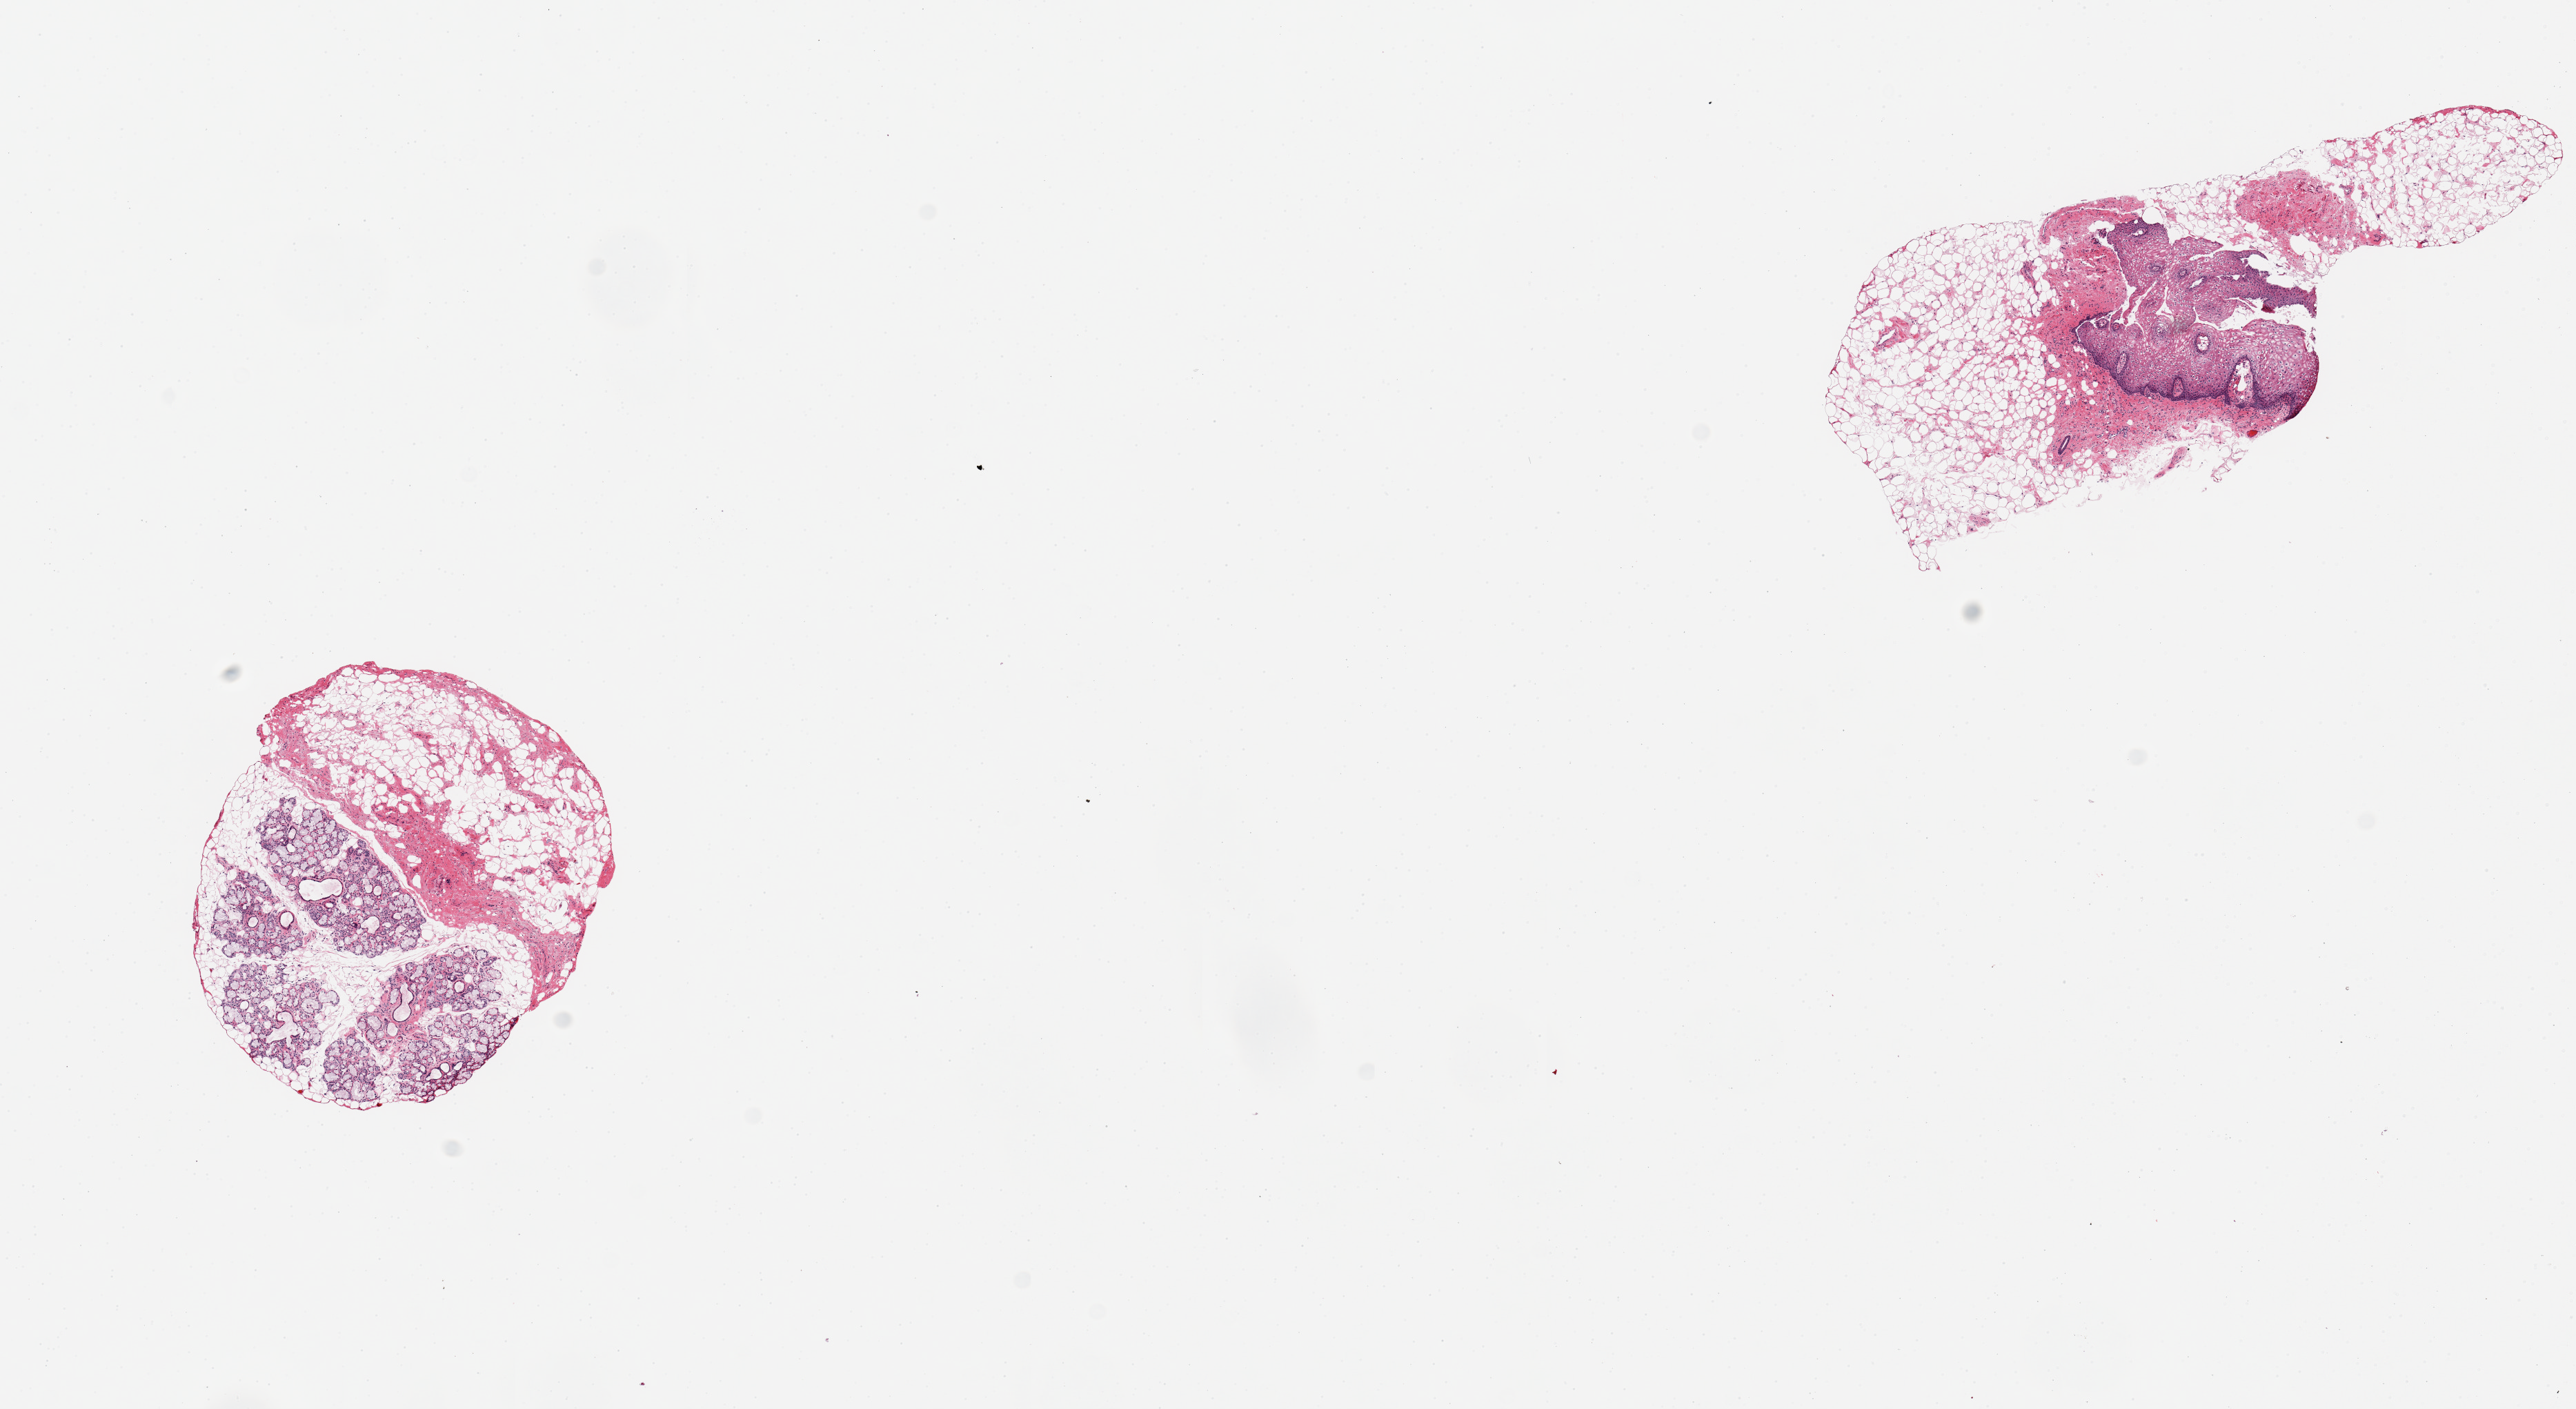
Whole-slide image, hematoxylin and eosin (H&E) stain, brightfield, whole scanned area (about 14.8 x 8.1 mm) shown as a low-resolution overview, PAXgene-fixed, paraffin-embedded tissue, sampled site (target tissue): minor salivary gland, tissue donor sample. Donor sex: female.
Reviewer comment on this tissue sample: 2 pieces; 1 piece has 50% salivary glands, 50% fat; other contains only fibrofatty stroma and epidermis, no glands.